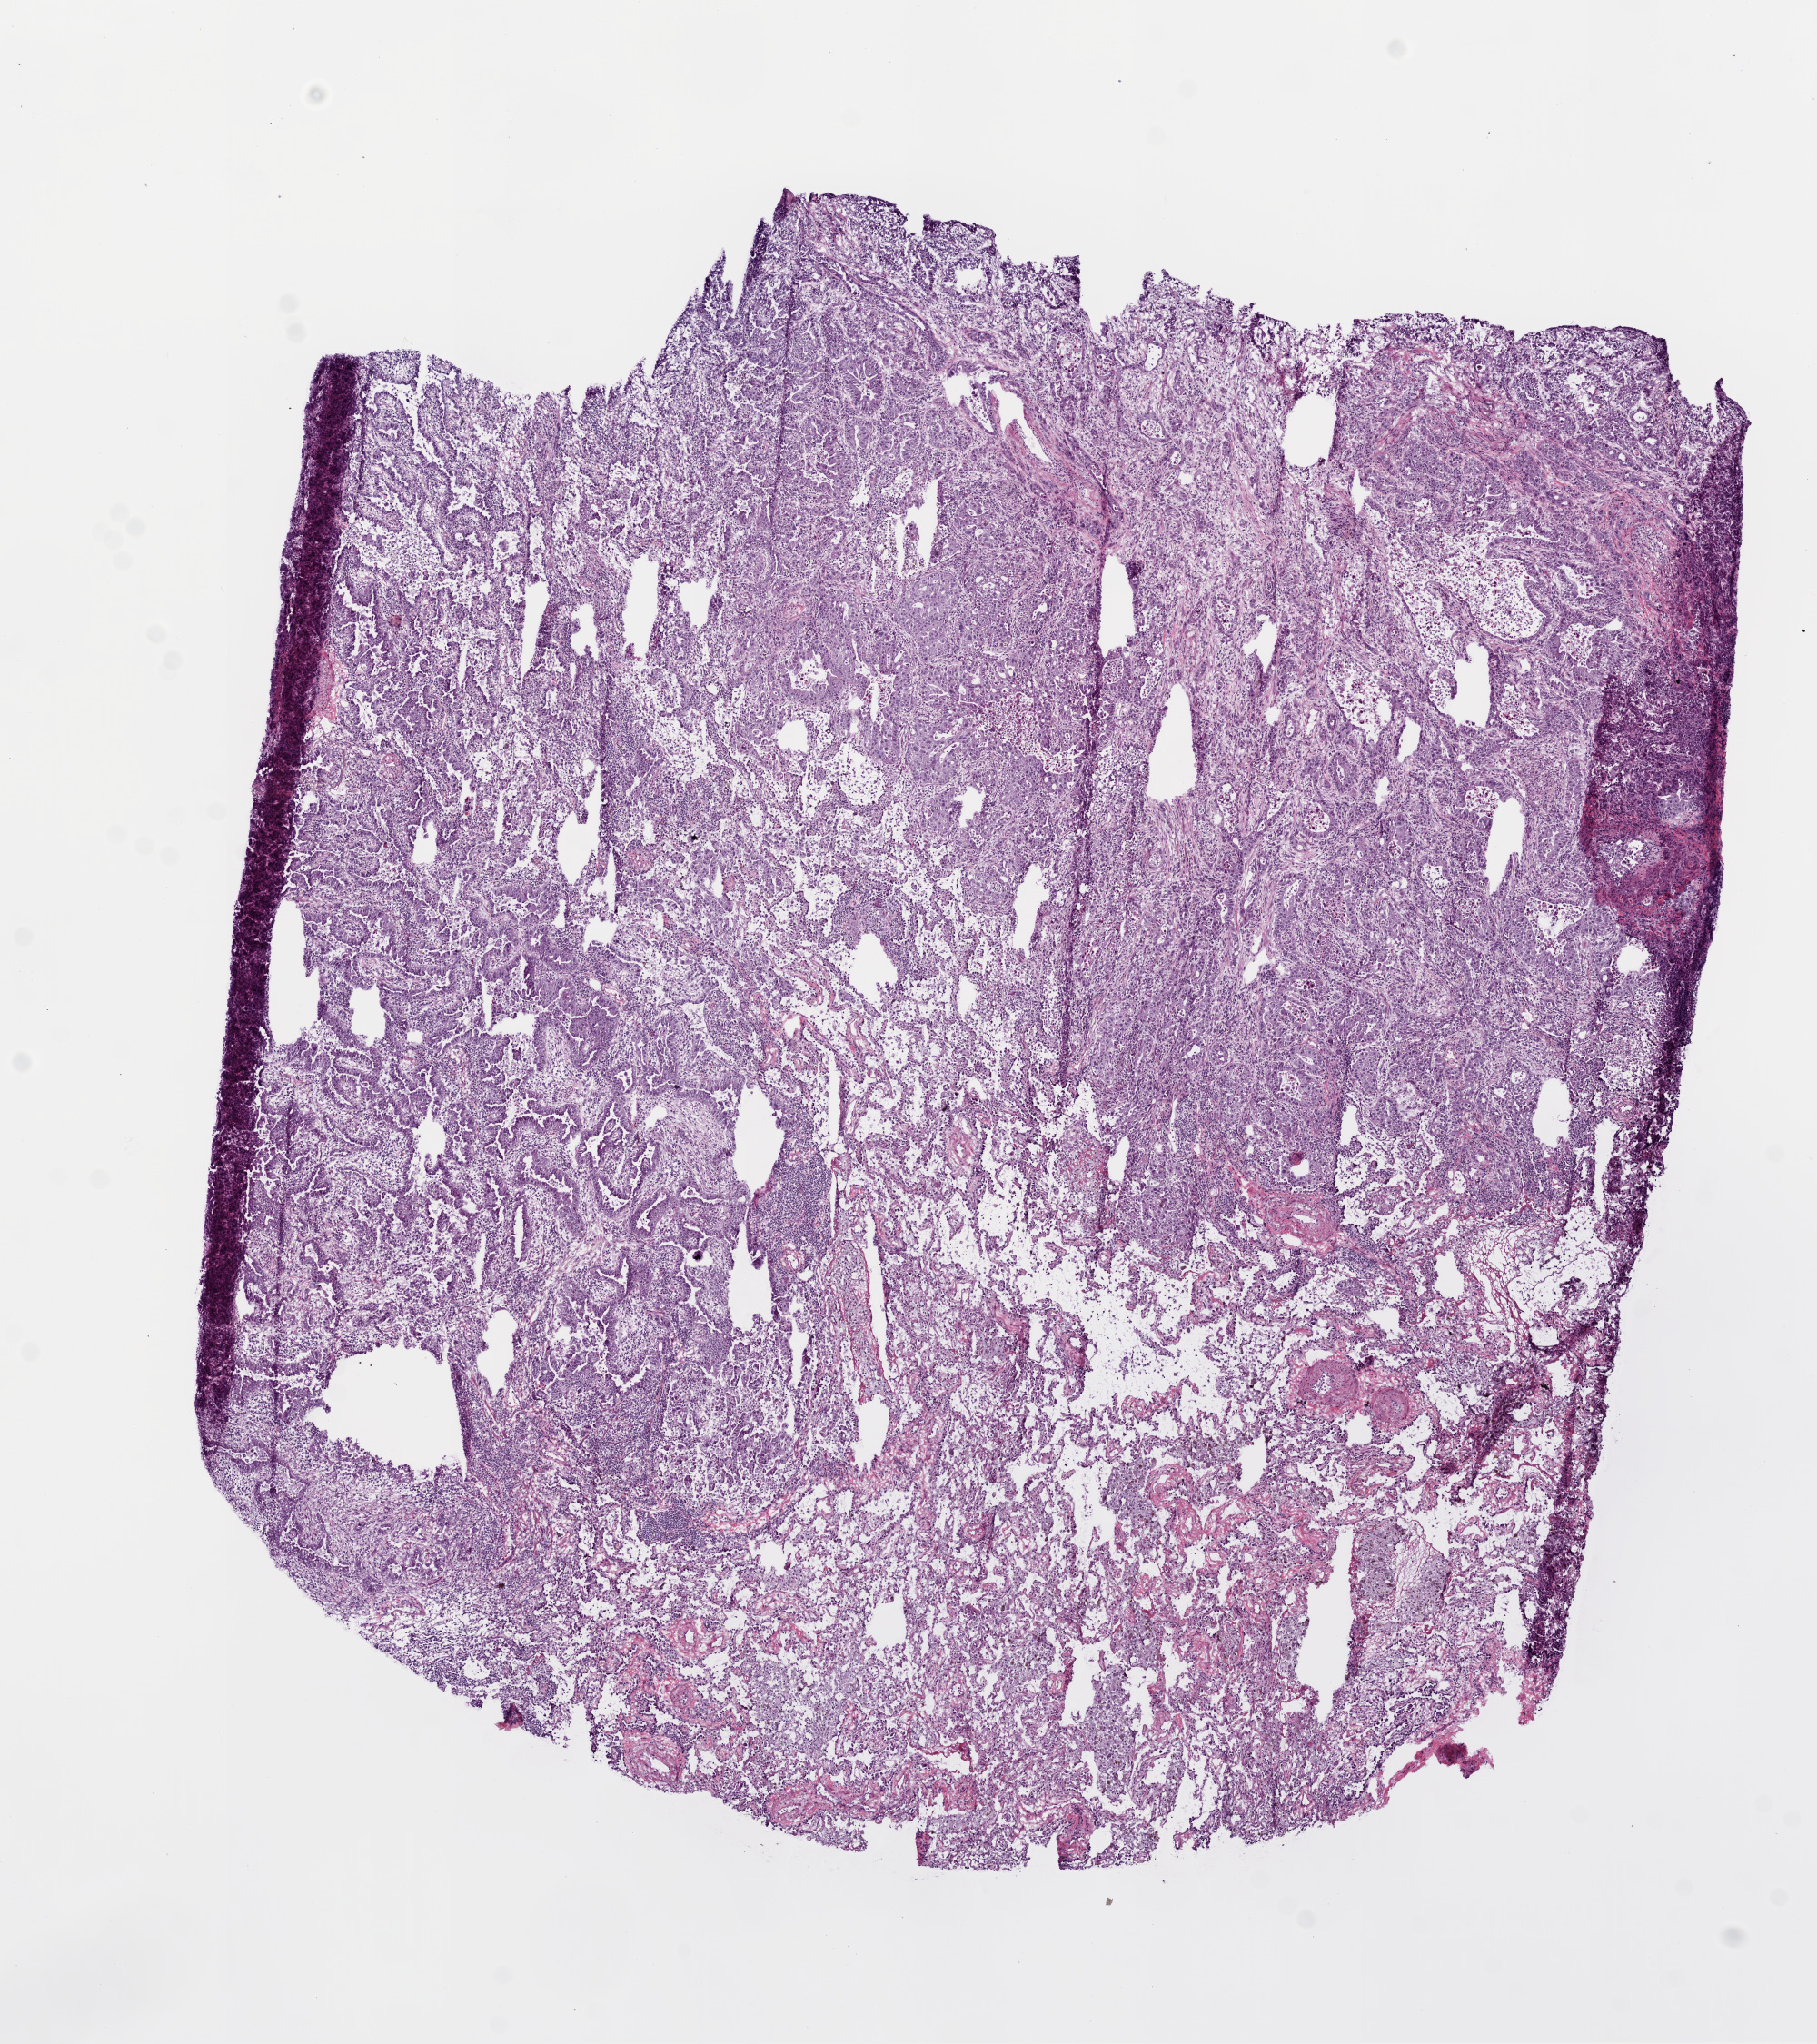
Digitized H&E tissue section (whole slide), shown as a low-resolution overview of the whole scanned area (about 8.0 x 9.0 mm, acquisition: 20x scan); frozen section; primary tumour sample from the lung. Male patient; age at initial diagnosis 68 years. Composition of this section per pathologist review: tumour cells 70%, tumour nuclei 60%, normal cells 25%, stromal cells 0%, necrosis 5%. Inflammatory infiltration, as recorded: lymphocyte infiltration 17%, monocyte infiltration 2%, neutrophil infiltration 20%.
• histologic diagnosis: Adenocarcinoma with mixed subtypes
• AJCC pathologic stage: IIB (7th edition)
• laterality: right